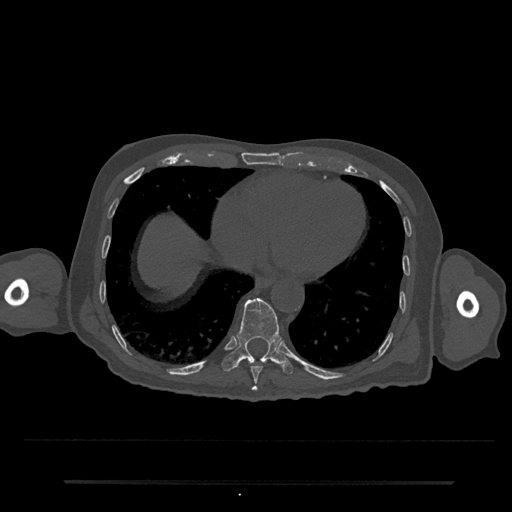
CT including the spine, one axial slice. Position 329 of 797 along the scan axis. 120 kVp. Bone window (W 1800 / L 400 HU). 0.5 mm slice thickness. 512 × 512 image matrix. Male patient, age 74 years. Case-level facts recorded for this patient, not image findings: primary cancer: prostate.
Outlined on this slice (semi-automatically segmented with operator editing):
- T10 vertebra: bounding box <222,298,293,375> (left, top, right, bottom; pixels)
- T9 vertebra: <250,362,263,391>